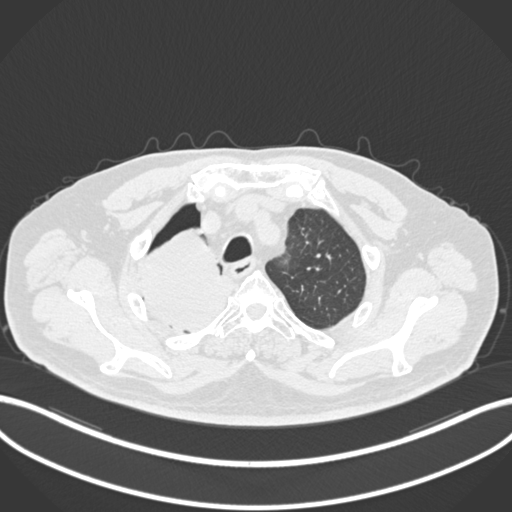
Chest CT, one axial slice; position 175 of 218 along the scan axis; 120 kVp; lung window (W 1500 / L -600 HU); 1 mm slice thickness; 512 × 512 image matrix, field of view 400 × 400 mm. Patient: male, 68 years. Case-level facts recorded for this patient, not image findings: clinical TNM (as recorded): T2a N0 M0.
Structures marked on this image (rectangle marked by the reading radiologist):
- lung tumour (recorded histology: adenocarcinoma): bounding box [x1, y1, x2, y2] px = [137, 231, 237, 336]